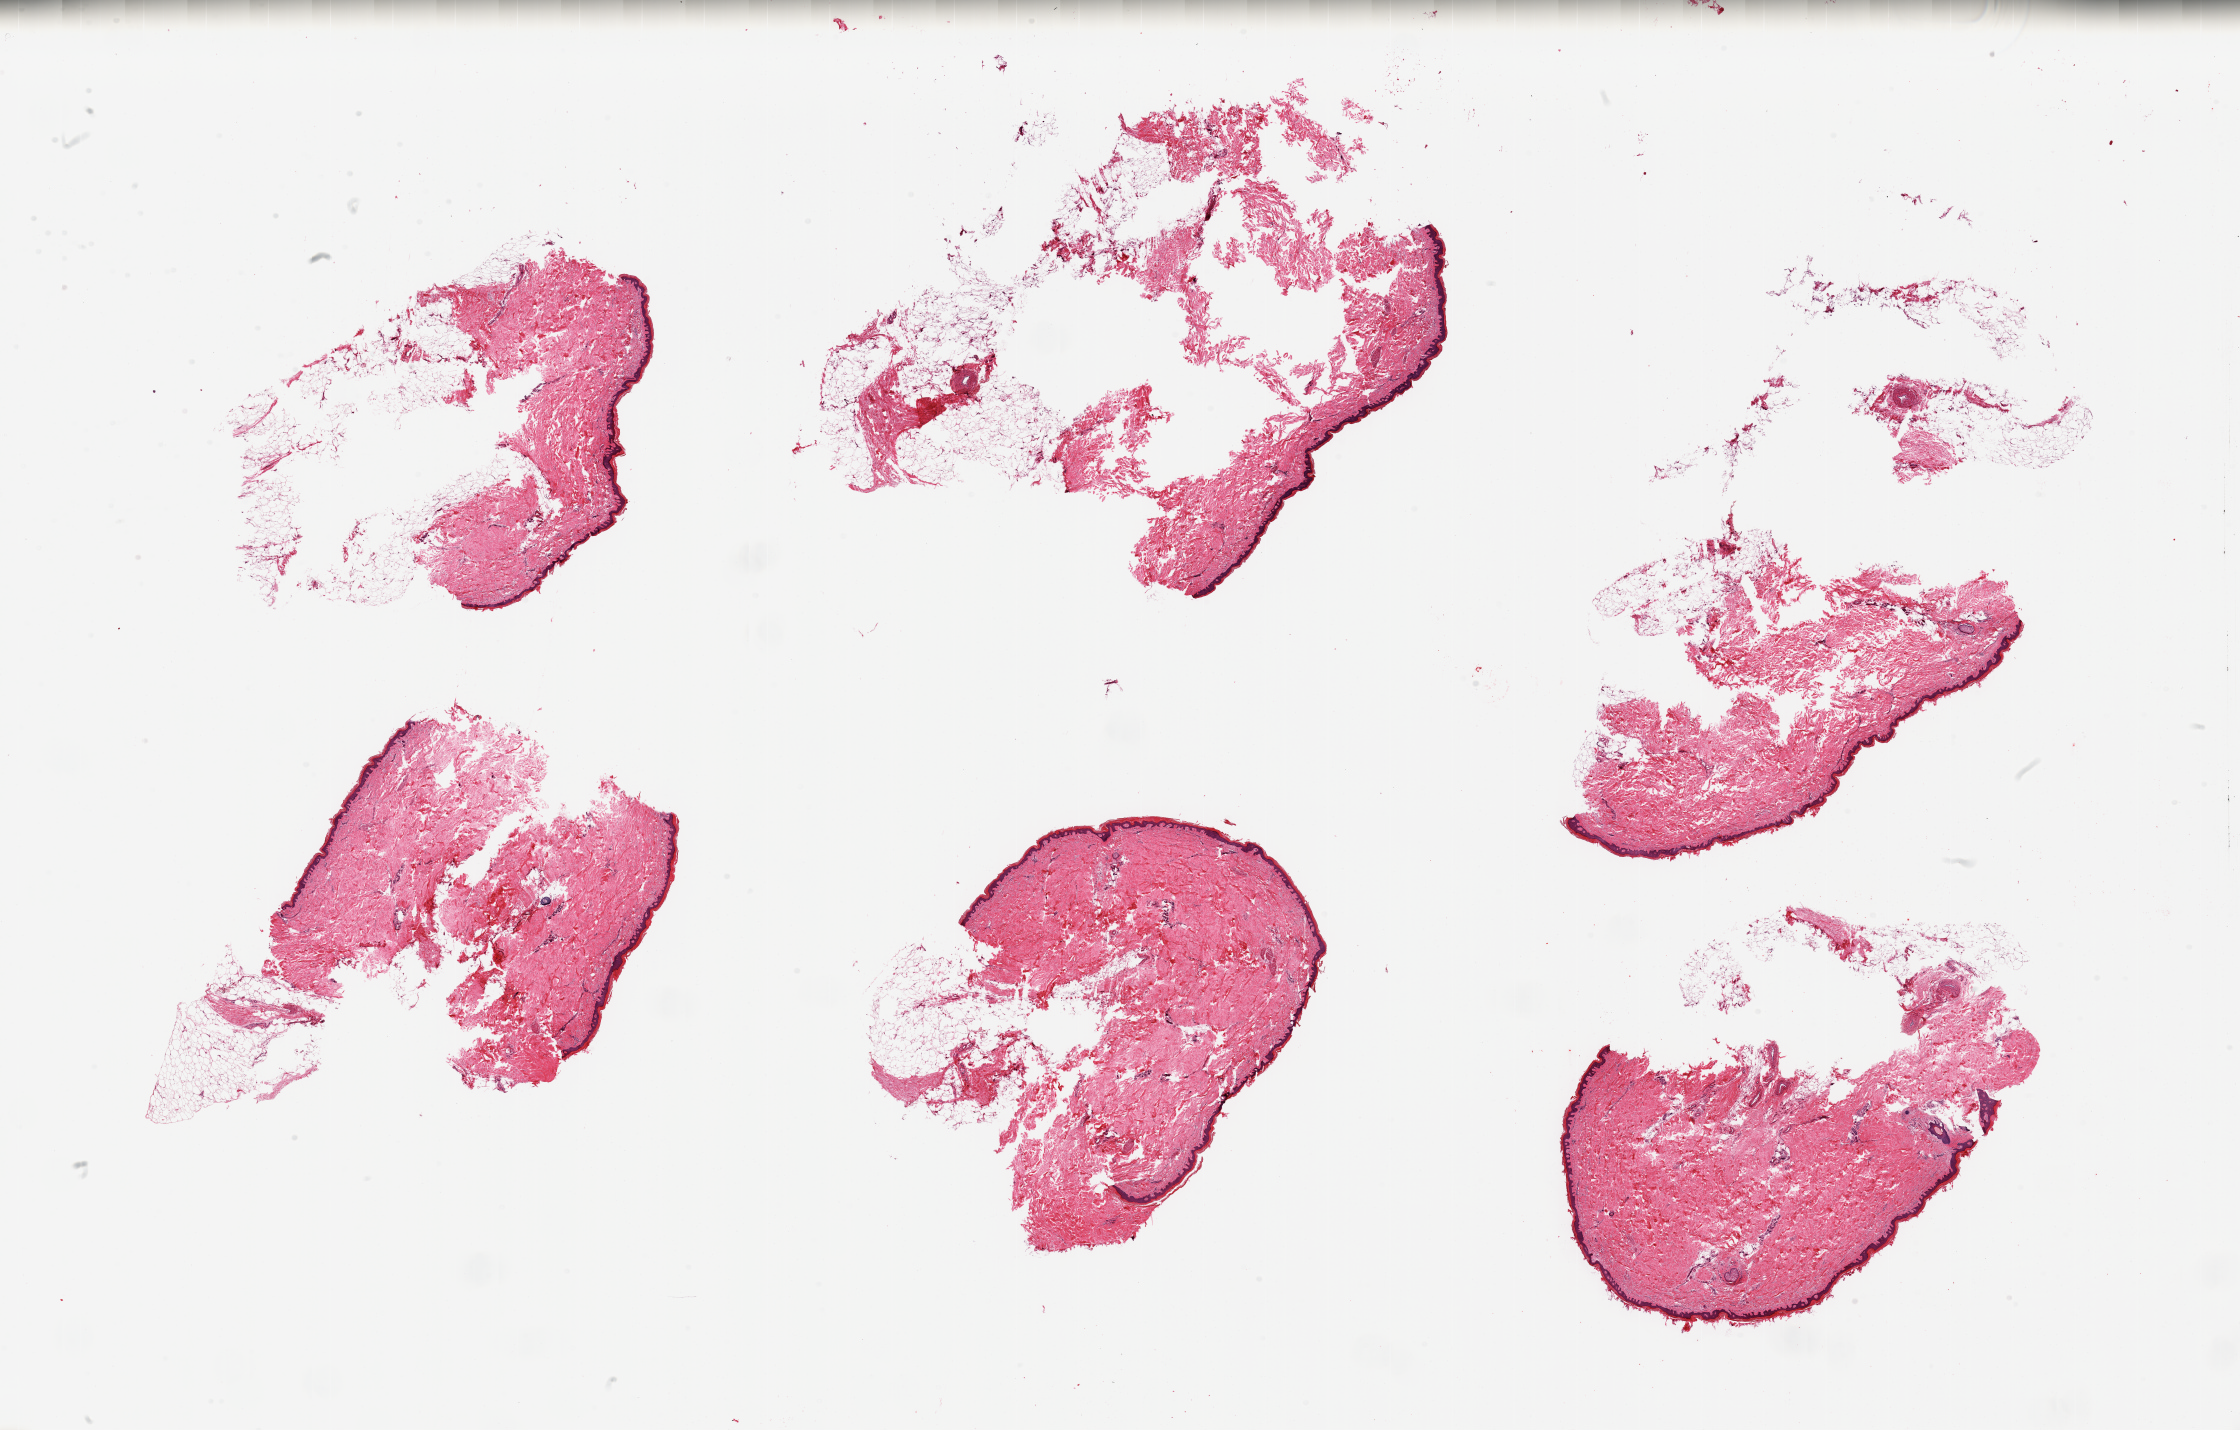
Whole-slide image, hematoxylin and eosin (H&E) stain, brightfield — shown as a low-resolution overview of the whole scanned area (about 35.4 x 22.6 mm), PAXgene-fixed paraffin-embedded (PFPE) section, target tissue: skin of lower leg, tissue donor sample. Male donor.
Pathologist's review note for this sample: 6 pieces, minimal fat, squamous epithelium is ~60 microns.